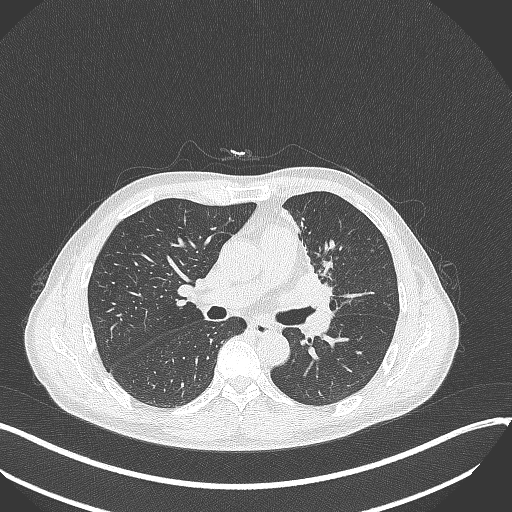
Chest CT, one axial slice; slice 189 of 411 in the series (ordered by position); reconstruction kernel B70f; 120 kVp; lung window (W 1500 / L -600 HU); 1 mm slice thickness; 512 × 512 image matrix. Male patient, age 56 years. Case-level facts recorded for this patient, not image findings: clinical TNM (as recorded): T2a N0 M0.
Annotated regions visible in this slice (bounding box drawn by a radiologist):
- lung tumour (recorded histology: squamous cell carcinoma): bounding box [x1, y1, x2, y2] px = [272, 266, 349, 311]